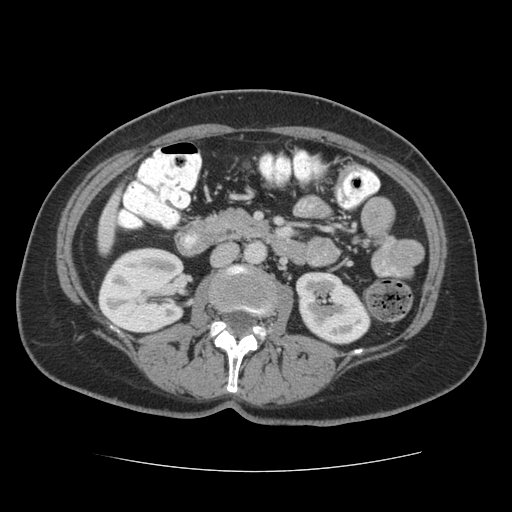
Contrast-enhanced abdominal CT (liver protocol), one axial slice. Slice 11 of 75 in the series (ordered by position). Reconstruction kernel STANDARD. Soft-tissue window (W 400 / L 40 HU). 2.5 mm slice thickness. 512 × 512 image matrix. From the clinical record (not read from this slice): diagnosis: hepatocellular carcinoma (patient treated with transarterial chemoembolisation; whether this scan precedes or follows treatment is not stated here); TNM stage (as recorded): Stage-I.
Annotated regions visible in this slice (semi-automatic segmentation, software-assisted and operator-edited):
- liver parenchyma outside the tumour (the mass and vessels are separate outlines, so this box may not span the whole liver): box from (x=98, y=210) to (x=114, y=252) px